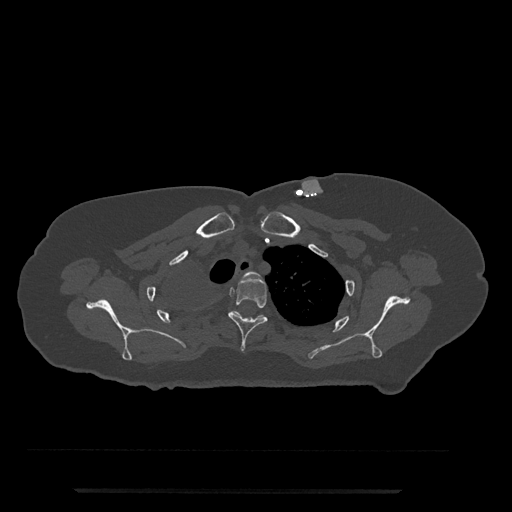
CT including the spine, one axial slice; reconstruction kernel Br40s/3; 120 kVp; bone window (W 1800 / L 400 HU); 512 × 512 image matrix, field of view 440 × 440 mm. Patient: female, 51 years. Case-level facts recorded for this patient, not image findings: primary cancer: neuro; vertebrae with lytic lesions (as recorded): T8.
Annotated regions visible in this slice (semi-automatically segmented with operator editing):
- T2 vertebra: bounding box (x1, y1, x2, y2) in pixels: (244, 271, 258, 277)
- T3 vertebra: (228, 273, 268, 353)
- T4 vertebra: (233, 311, 264, 318)